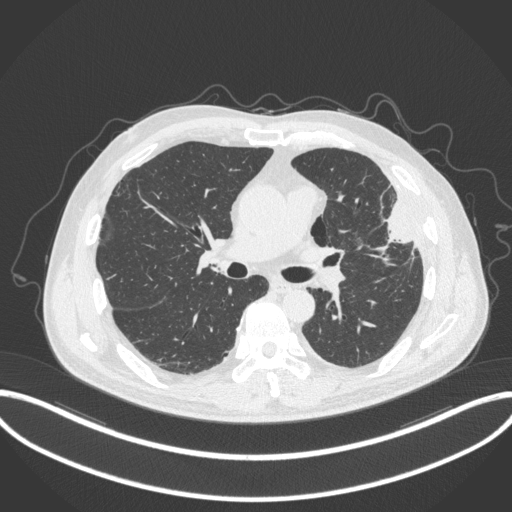
Chest CT, one axial slice; reconstruction kernel B31f; 120 kVp; lung window (W 1500 / L -600 HU); 1 mm slice thickness; 512 × 512 image matrix, field of view 415 × 415 mm. Patient: male, 64 years. Case-level facts recorded for this patient, not image findings: clinical TNM (as recorded): T4 N1 M0; histopathological grade: G3.
Structures marked on this image (rectangle marked by the reading radiologist):
- lung tumour (recorded histology: adenocarcinoma): box from (x=379, y=196) to (x=414, y=250) px